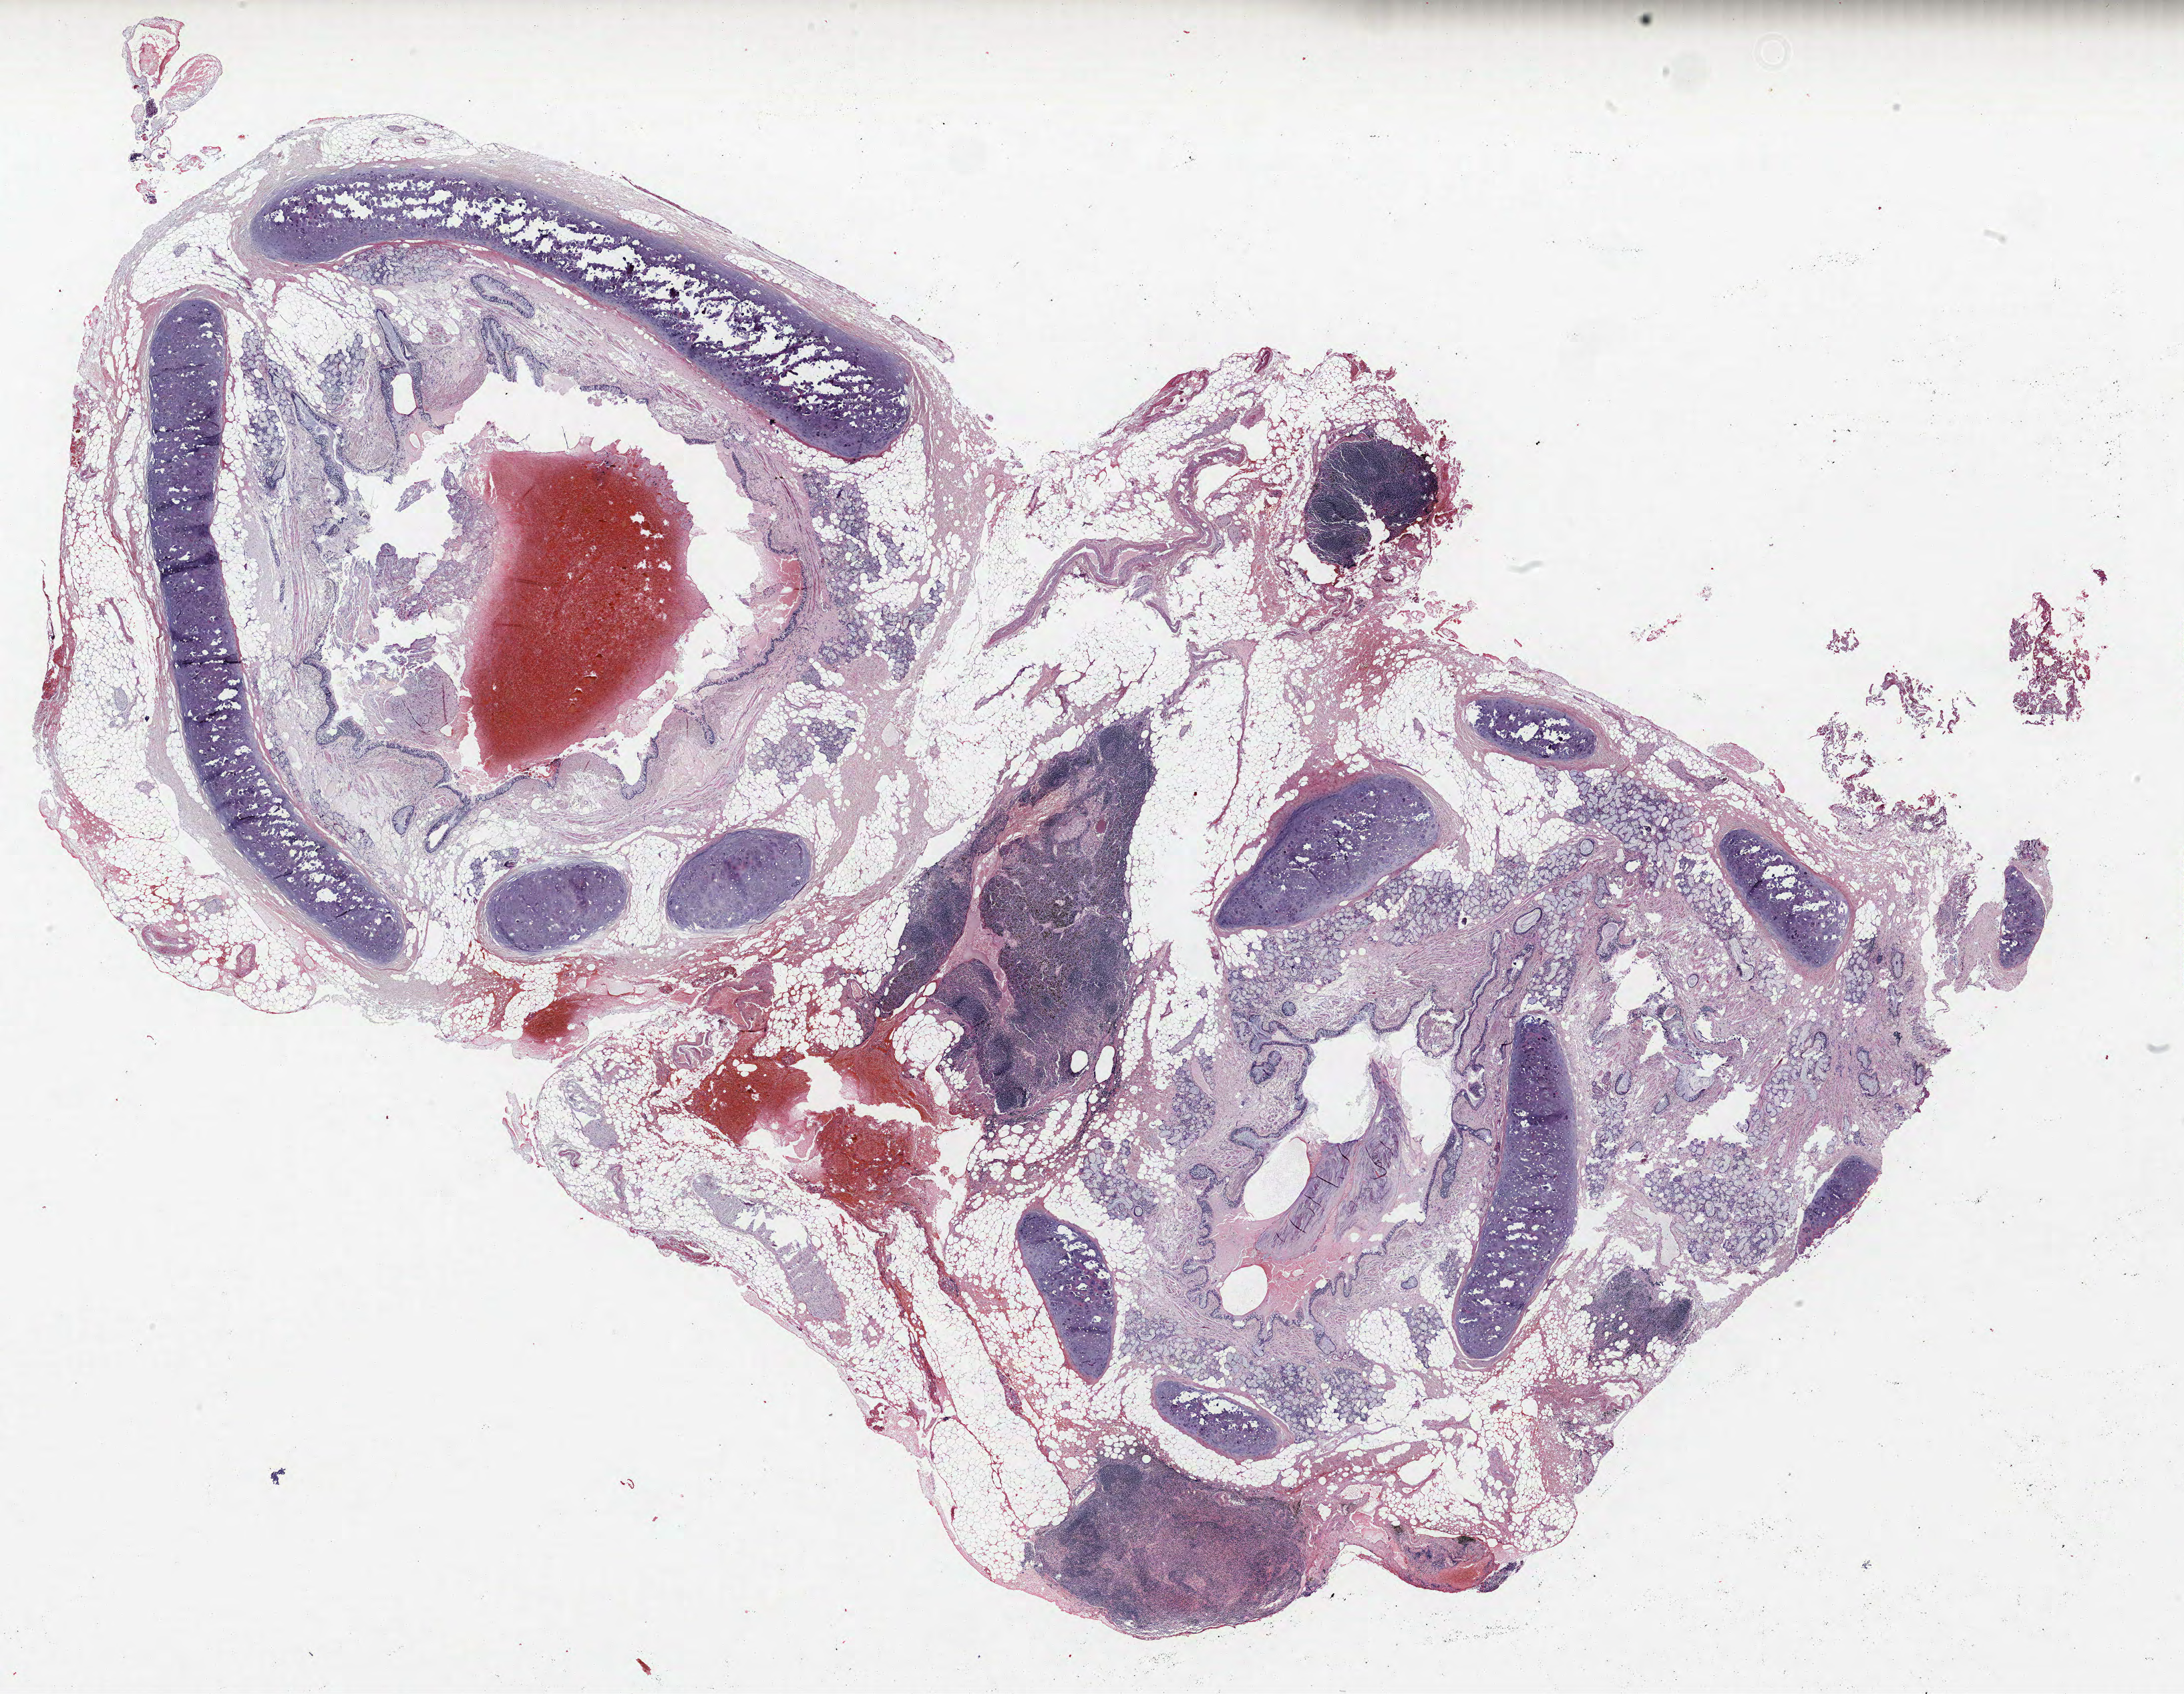
H&E whole-slide image, shown as a low-resolution overview of the whole scanned area (about 26.2 x 20.3 mm, from a 40x scan), FFPE section, lung. Male patient, aged 73 at enrolment. Current smoker at enrolment. Grade: poorly differentiated (G3).
• tumour size (pathology): 12 mm
• primary tumour location (clinical record): left lower lobe
• participant's lung-cancer diagnosis: Adenocarcinoma, NOS
• ICD-O-3 topography: lower lobe of lung (C34.3)
• stage (AJCC 6th edition): IIA